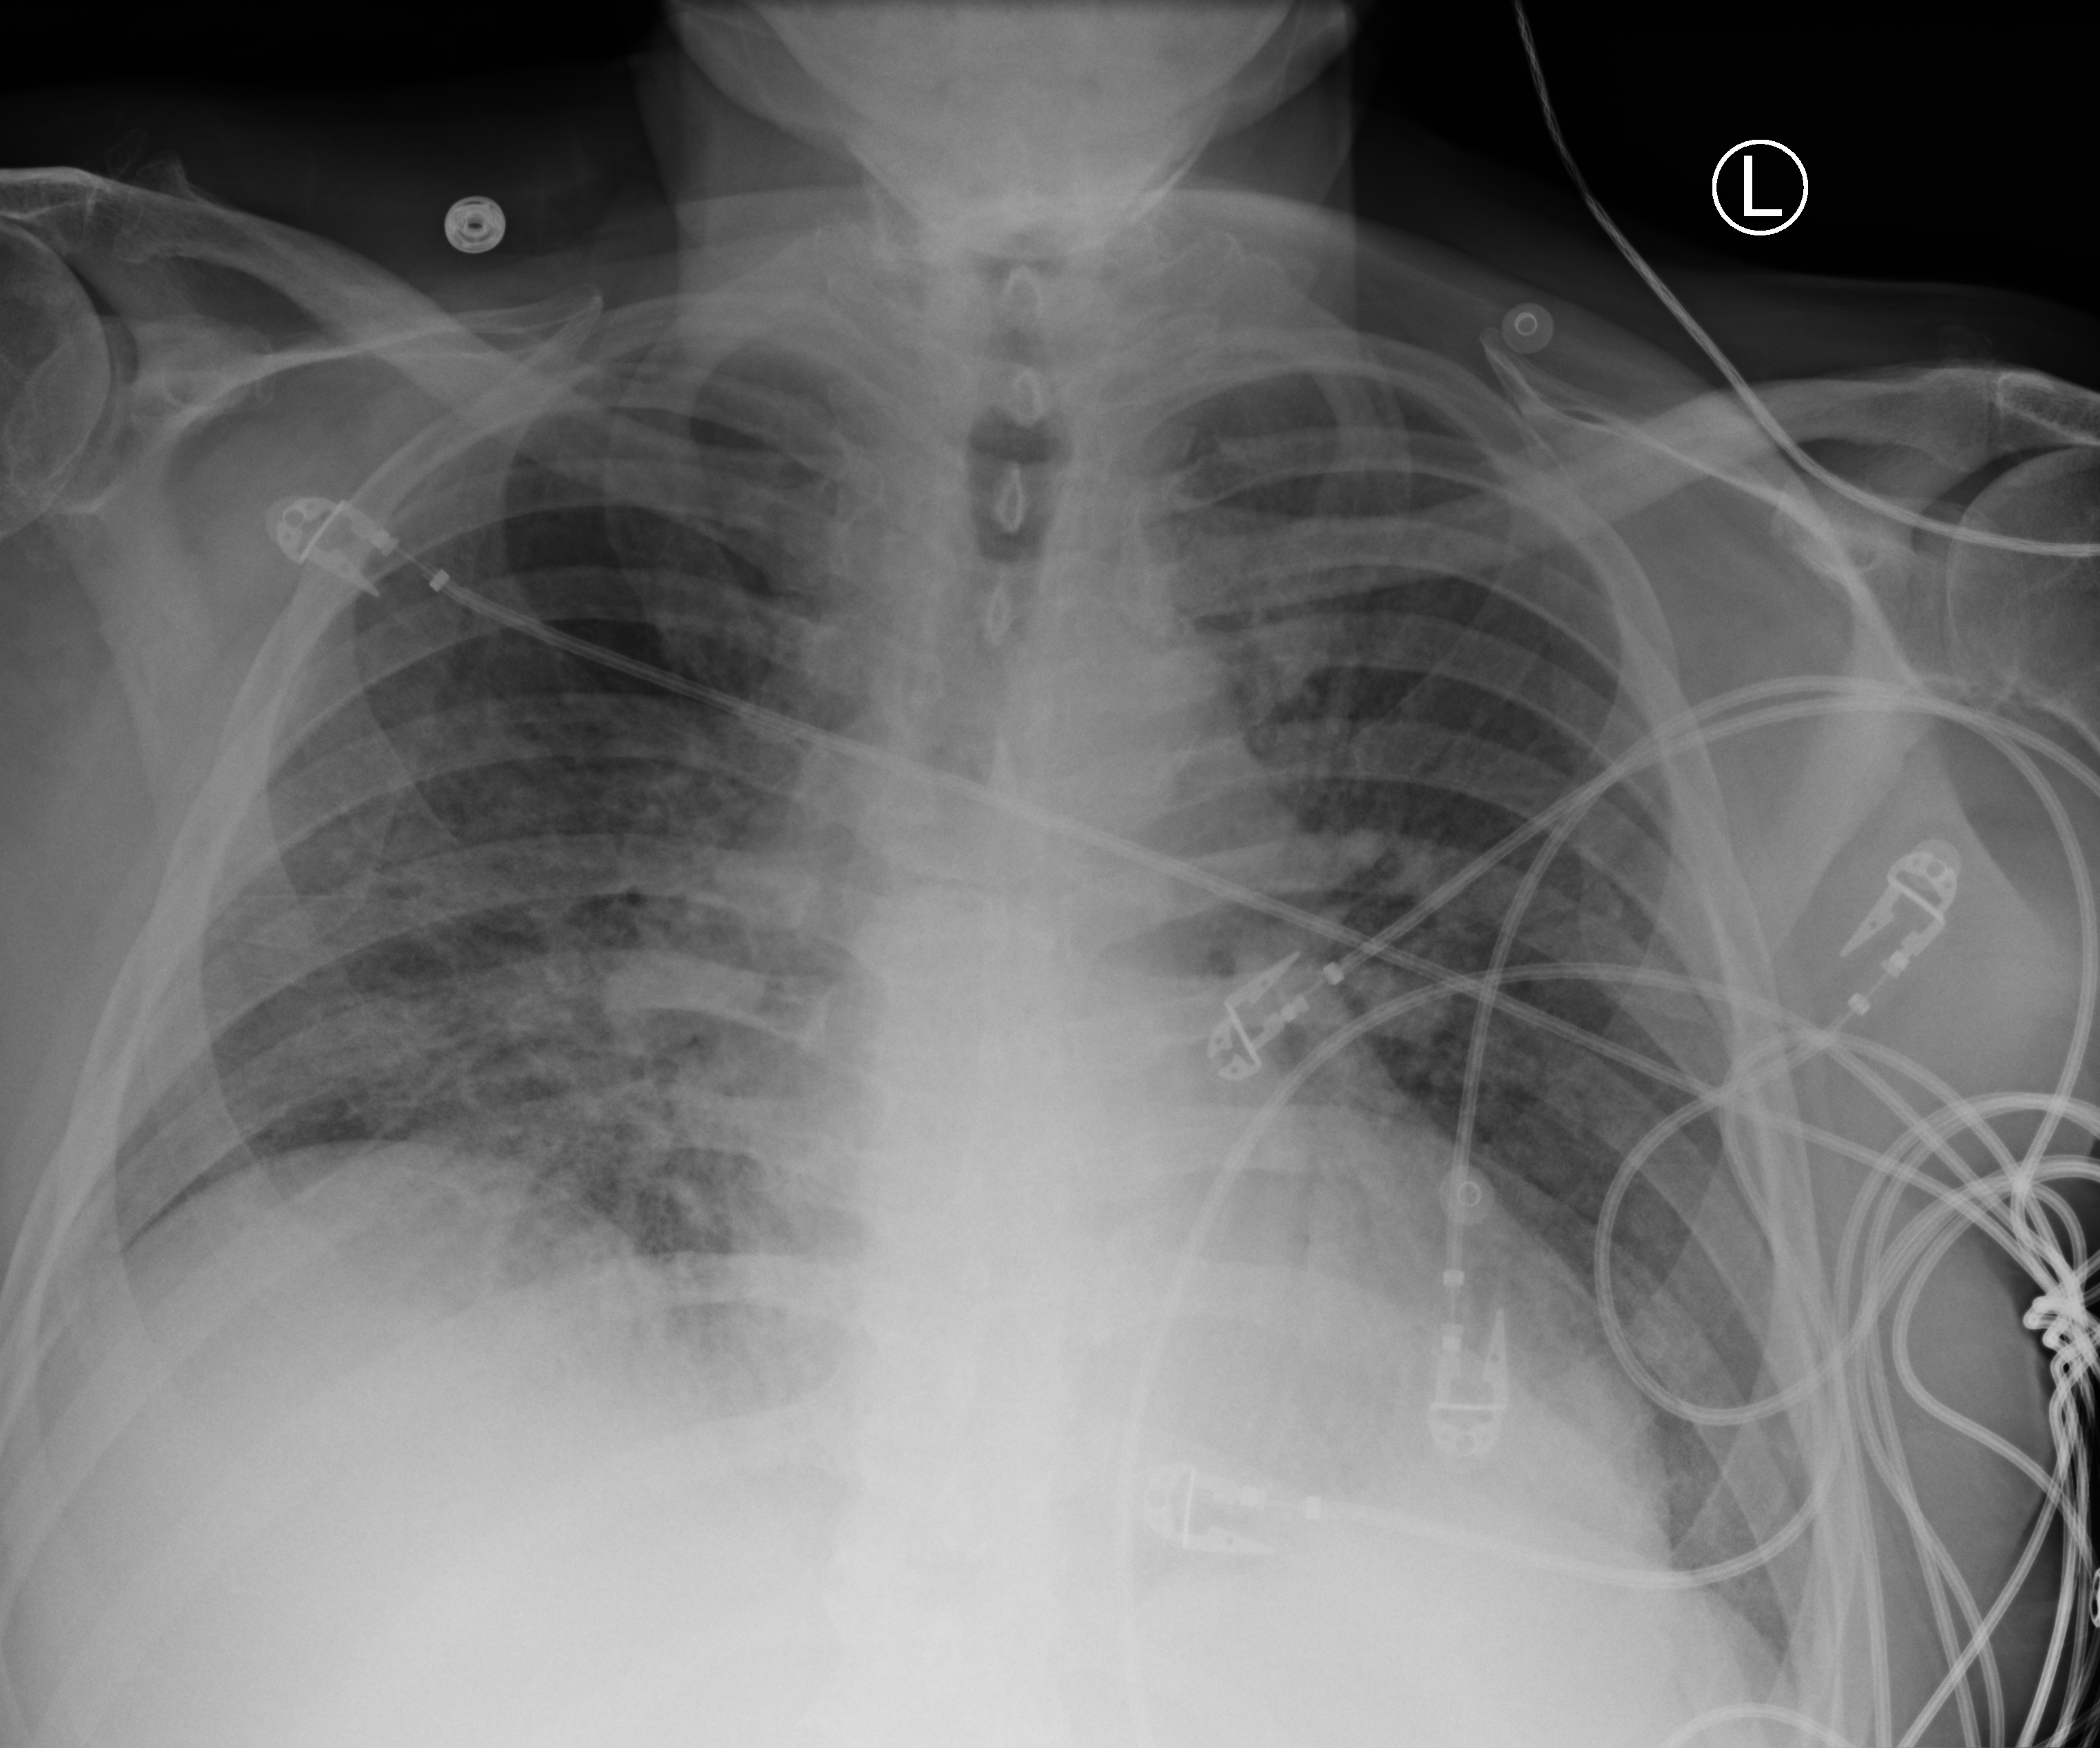
Bedside chest radiograph (computed radiography); anteroposterior (AP) projection. Patient hospitalised with COVID-19; male, aged 60–74 years.
From the hospital-stay record, not from the radiograph (when in the stay this image was taken is not recorded): mechanically ventilated during this hospital stay: yes.